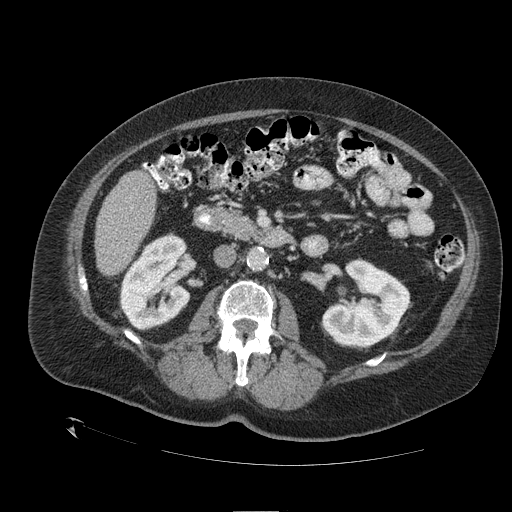
Contrast-enhanced abdominal CT (liver protocol), one axial slice. Position 42 of 109 along the scan axis. 120 kVp. One of 2 acquisitions stored at this slice position. Soft-tissue window (W 400 / L 40 HU). 2.5 mm slice thickness. 512 × 512 image matrix, field of view 460 × 460 mm. Case-level facts recorded for this patient, not image findings: diagnosis: hepatocellular carcinoma (patient treated with transarterial chemoembolisation; whether this scan precedes or follows treatment is not stated here); TNM stage (as recorded): Stage-I; Child-Pugh class: A; tumour size: 4.6 cm.
Outlined on this slice (semi-automatically segmented with operator editing):
- liver parenchyma outside the tumour (the mass and vessels are separate outlines, so this box may not span the whole liver): bounding box <94,170,156,276> (left, top, right, bottom; pixels)